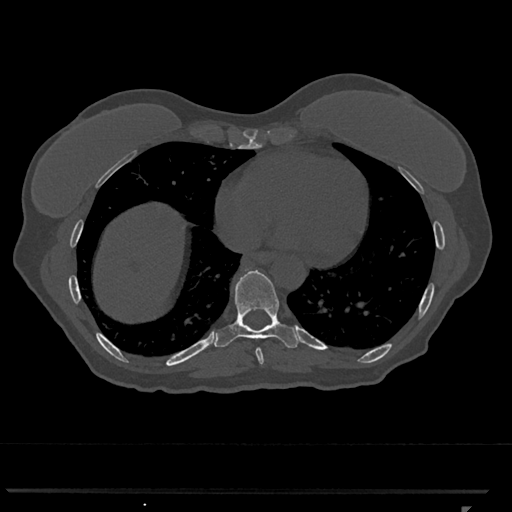
CT including the spine, one axial slice; slice 623 of 793 in the series (ordered by position); reconstruction kernel Br40s/3; bone window (W 1800 / L 400 HU); 0.5 mm slice thickness; 512 × 512 image matrix, field of view 380 × 380 mm. Female patient, age 62 years. From the clinical record (not read from this slice): primary cancer: renal.
Outlined on this slice (semi-automatically segmented with operator editing):
- T8 vertebra: box from (x=255, y=348) to (x=264, y=366) px
- T9 vertebra: (x=214, y=269)–(x=299, y=348)